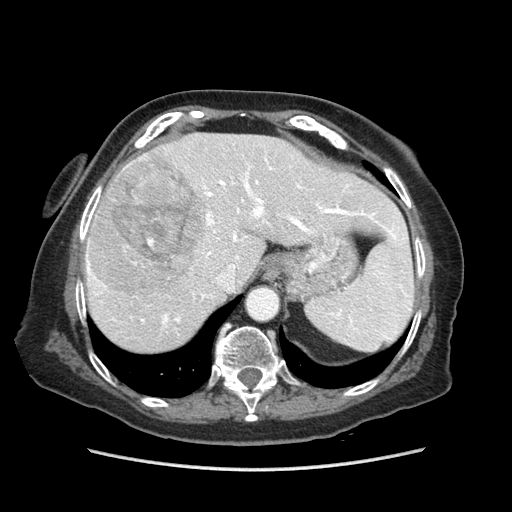
Contrast-enhanced abdominal CT (liver protocol), one axial slice; slice 62 of 89 in the series (ordered by position); reconstruction kernel STANDARD; 140 kVp; soft-tissue window (W 400 / L 40 HU); 2.5 mm slice thickness; 512 × 512 image matrix. Case-level facts recorded for this patient, not image findings: diagnosis: hepatocellular carcinoma (patient treated with transarterial chemoembolisation; whether this scan precedes or follows treatment is not stated here); TNM stage (as recorded): Stage-IIIA; Child-Pugh class: A; tumour nodularity: multinodular.
Annotated regions visible in this slice (semi-automatic segmentation, software-assisted and operator-edited):
- liver parenchyma outside the tumour (the mass and vessels are separate outlines, so this box may not span the whole liver): bounding box [x1, y1, x2, y2] px = [84, 132, 402, 352]
- mass: [88, 158, 211, 293]
- liver vessels: [86, 157, 395, 325]